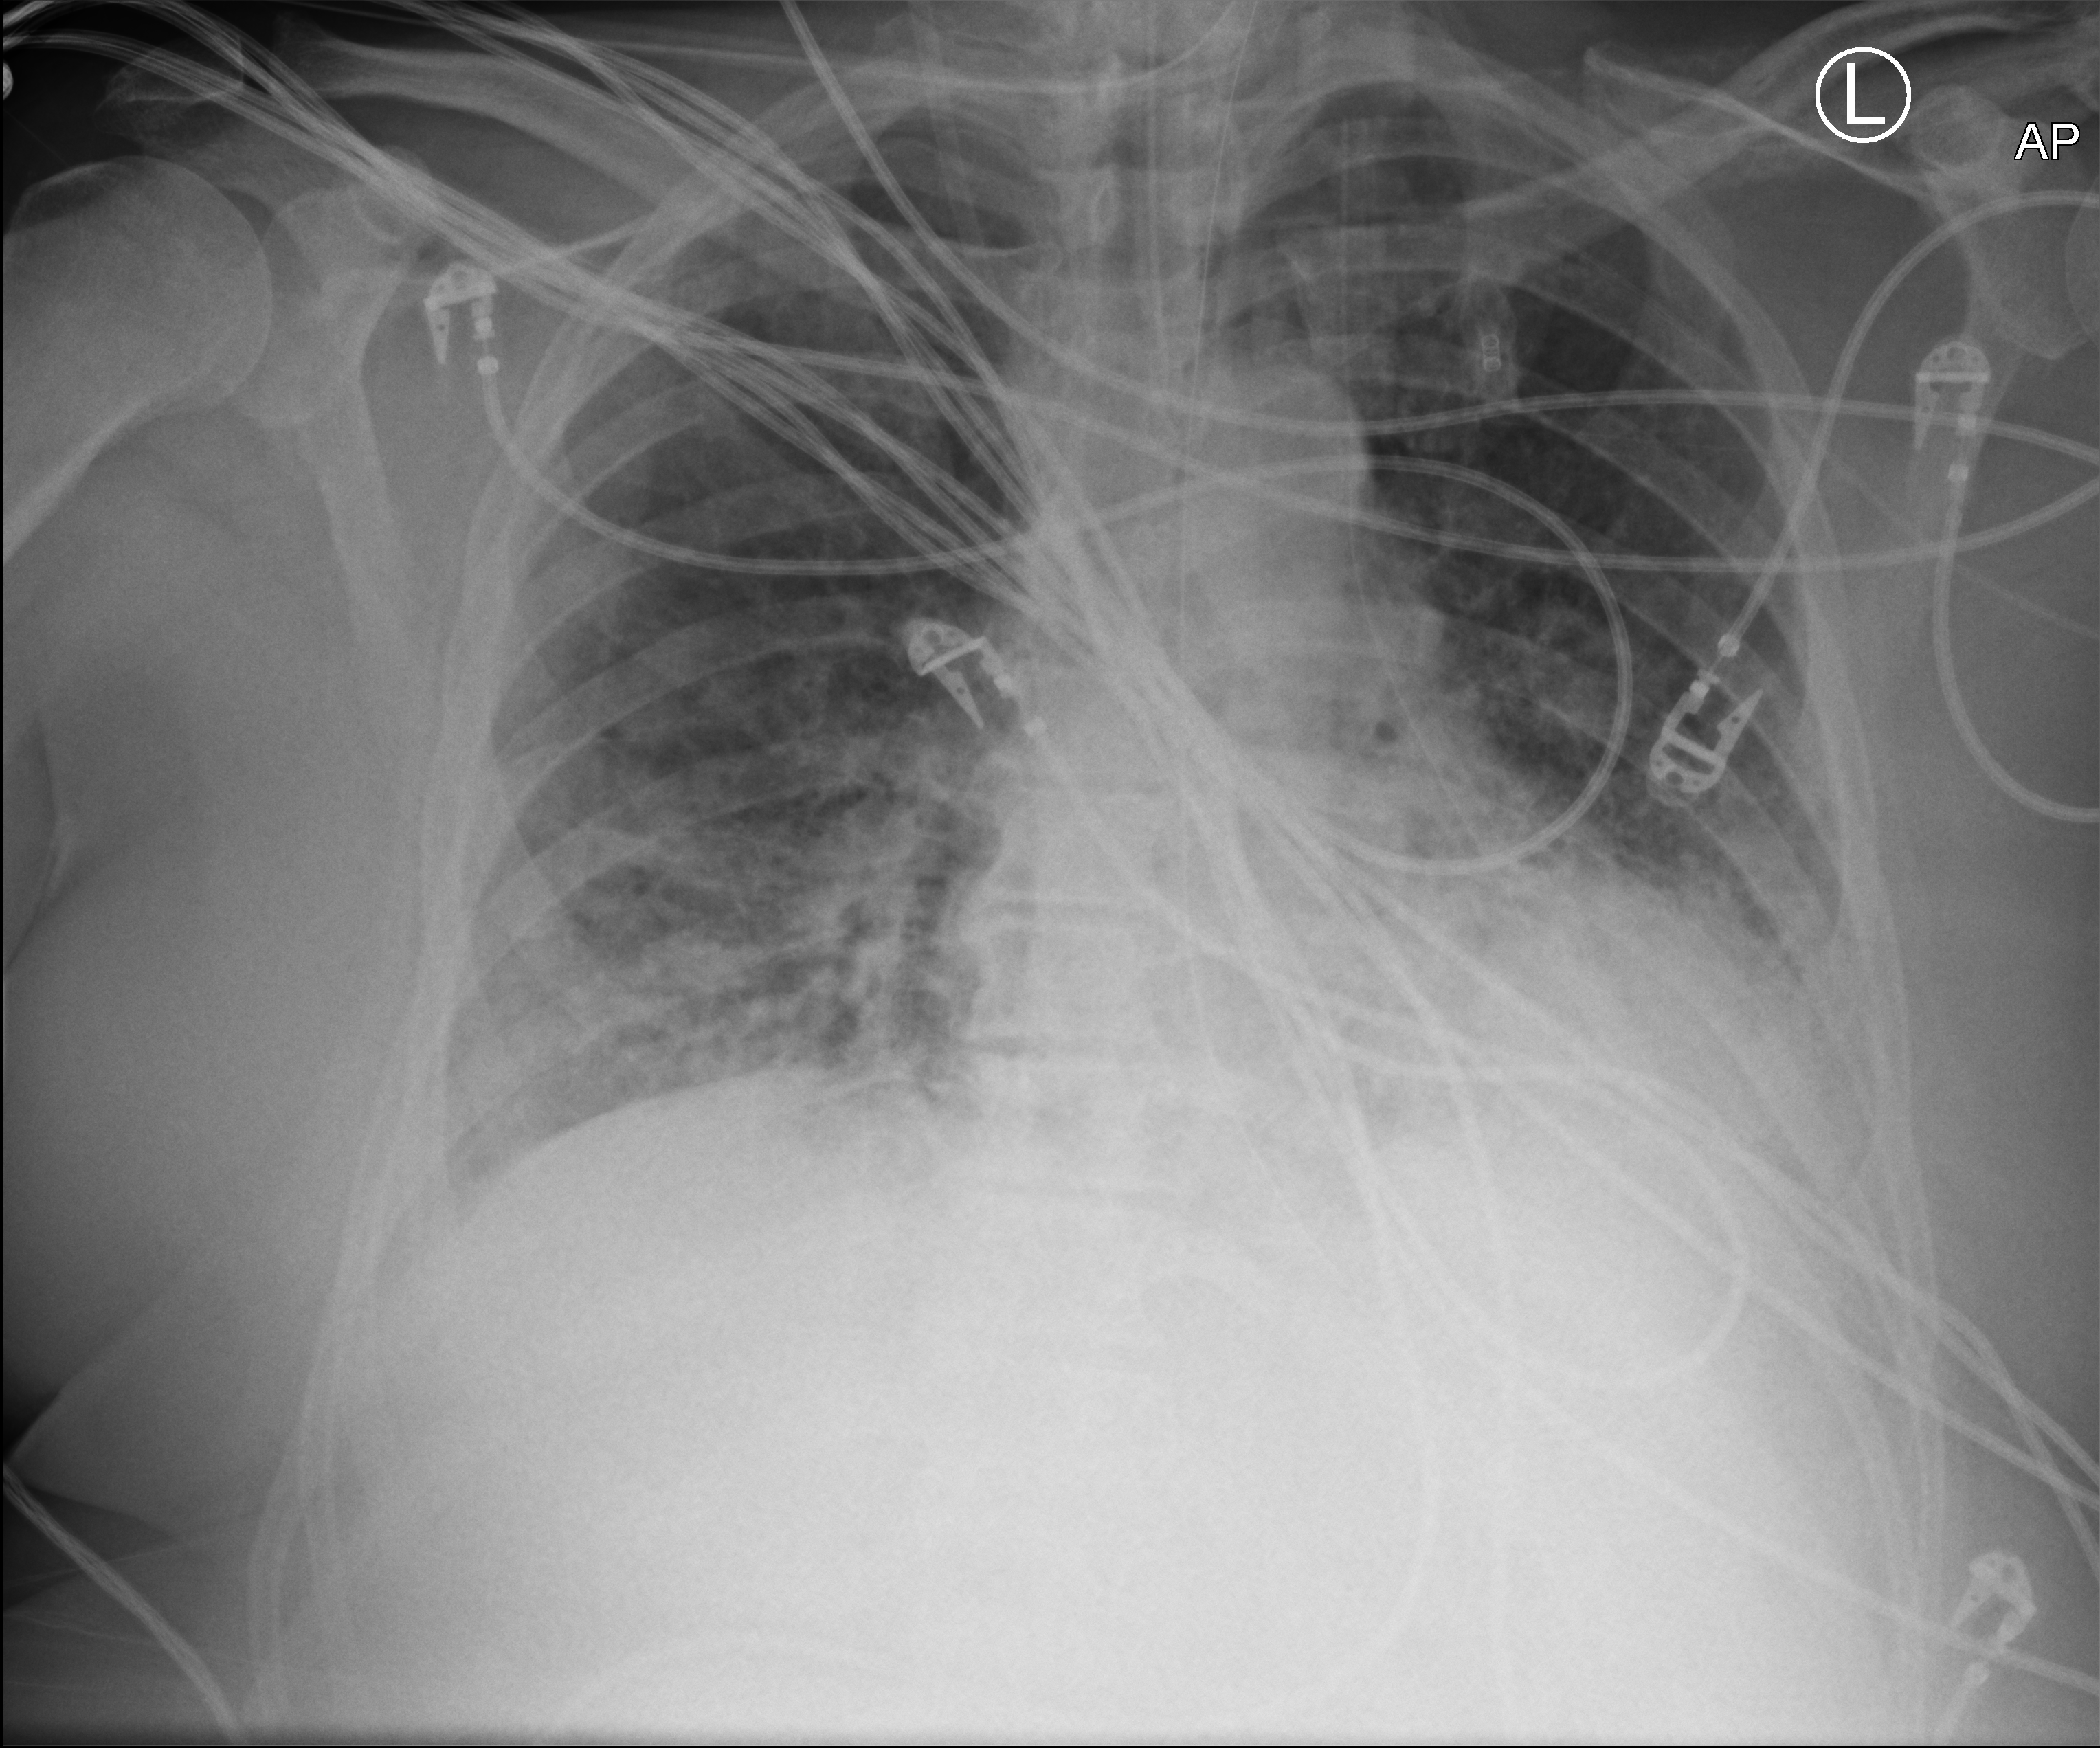
Bedside chest radiograph (computed radiography), anteroposterior (AP) projection. Male patient hospitalised with COVID-19, age 60–74 years.
Hospital-stay facts (about this admission, not read from this image; timing relative to this image not recorded):
- chronic kidney disease (admission record): no